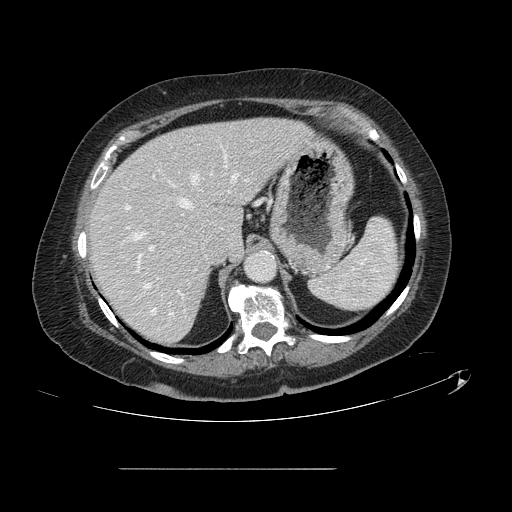
Contrast-enhanced abdominal CT, one axial slice. Slice 98 of 148 in the series (ordered by position). 120 kVp. Soft-tissue window (W 400 / L 40 HU). 2.5 mm slice thickness. 512 × 512 image matrix, field of view 439 × 439 mm. Female patient, age 75 years. Case-level facts recorded for this patient, not image findings: diagnosis: colorectal cancer liver metastases, imaged before liver resection; multiple liver metastases: no; largest metastasis: 2.4 cm; disease in both lobes: no.
Structures marked on this image (outlined manually by an expert reader):
- hepatic veins: box from (x=135, y=173) to (x=249, y=313) px
- liver: (x=90, y=118)–(x=306, y=344)
- planned liver remnant (the part of the liver to remain after resection): (x=90, y=118)–(x=308, y=344)
- portal vein (with intrahepatic branches): (x=126, y=175)–(x=180, y=293)